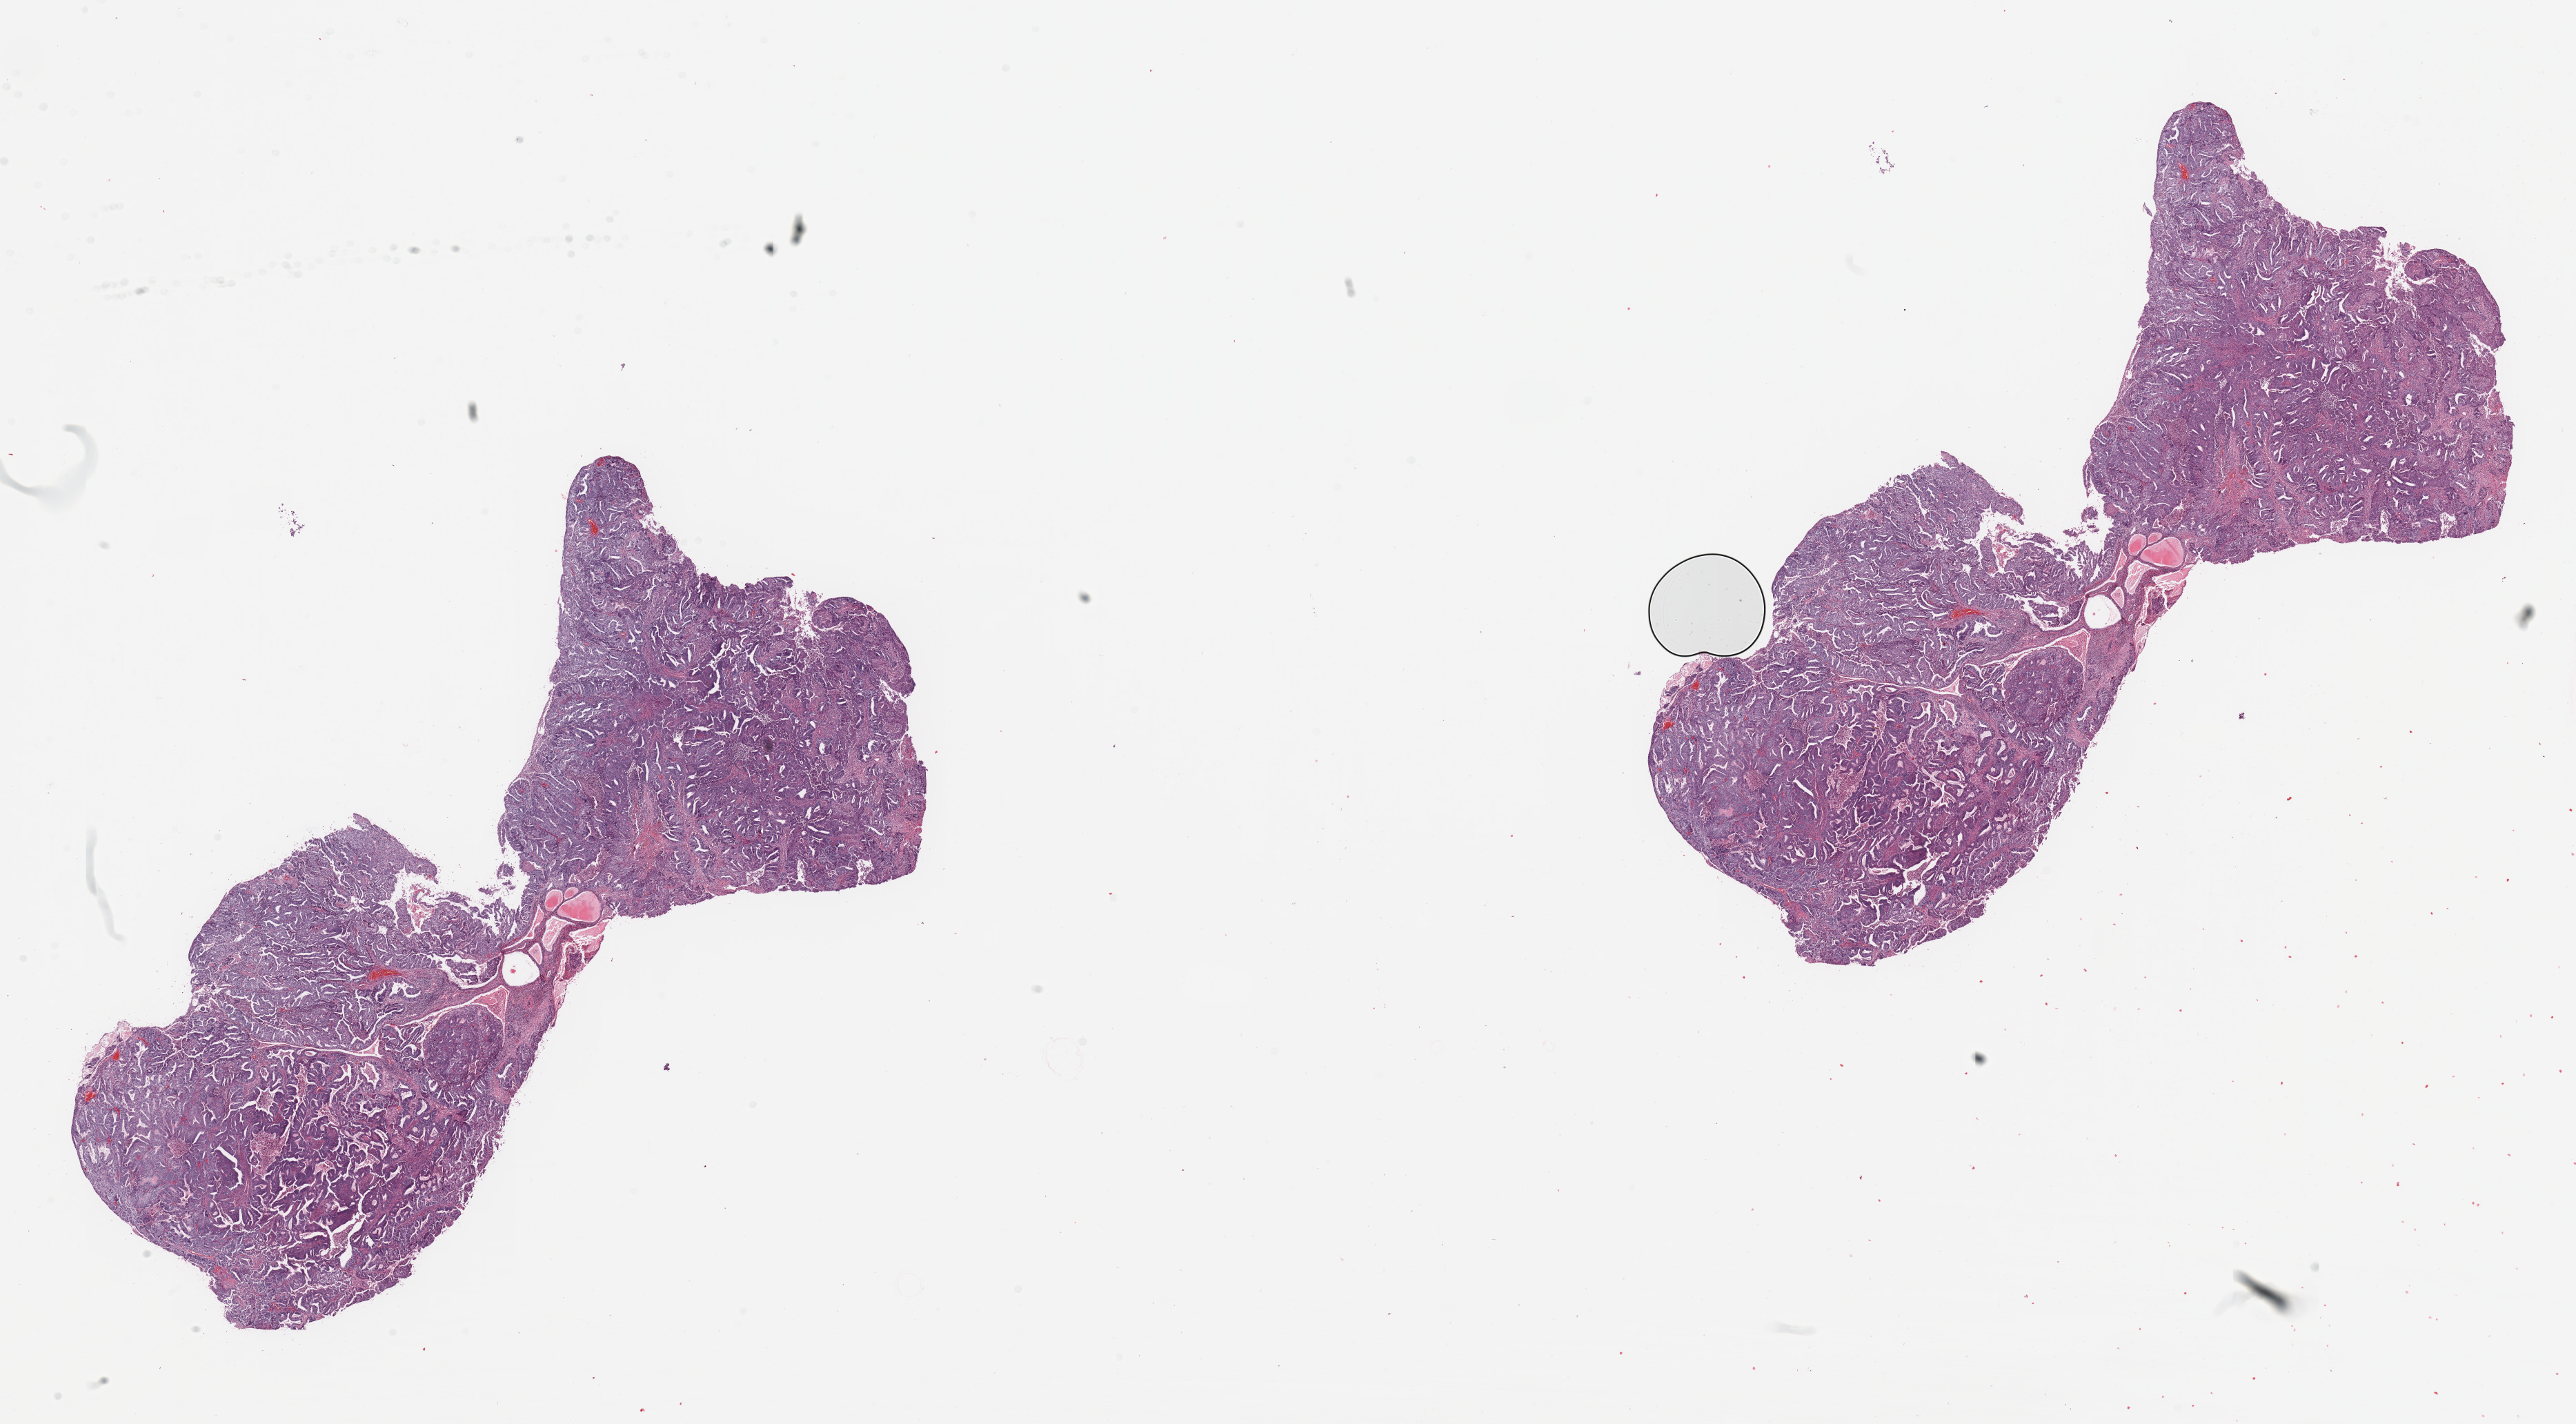
Digitized H&E-stained tissue section (whole slide), shown as a low-resolution overview of the whole scanned area (about 29.5 x 16.3 mm). Tumour tissue sample, uterus. 61-year-old female patient. Histologic grade: G2 (moderately differentiated).
Diagnosis: Endometrioid adenocarcinoma, NOS. AJCC pathologic stage: III.